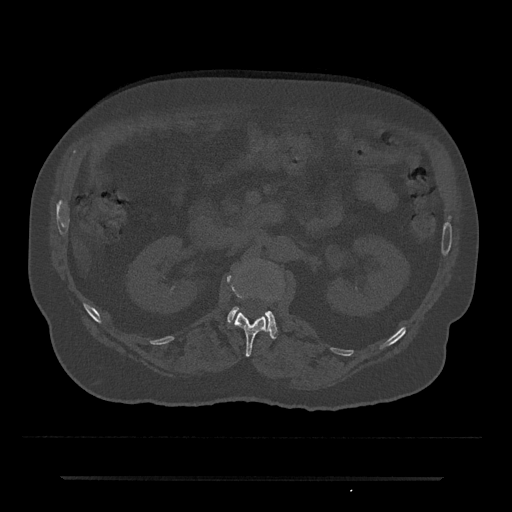
CT including the spine, one axial slice. Slice 46 of 797 in the series (ordered by position). Reconstruction kernel Br40s/3. 120 kVp. Bone window (W 1800 / L 400 HU). 0.5 mm slice thickness. 512 × 512 image matrix. Male patient, age 69 years. Case-level facts recorded for this patient, not image findings: primary cancer: prostate.
Annotated regions visible in this slice (semi-automatically segmented with operator editing):
- L1 vertebra: box from (x=227, y=275) to (x=267, y=357) px
- L2 vertebra: (x=227, y=307)–(x=278, y=339)